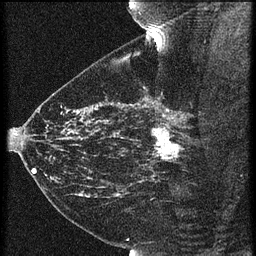
Breast MRI (dynamic contrast-enhanced), one sagittal slice; slice 42 of 60 in the series (ordered by position); 3 images stored at this slice position (order not interpretable as contrast timing); 1.5 T; TE 4.2 ms, TR 21.3 ms; 1.5 mm slice thickness; 256 × 256 image matrix, field of view 180 × 180 mm. Female patient, age 43 years. Case-level facts recorded for this patient, not image findings: setting: breast cancer imaged before/during neoadjuvant chemotherapy; receptor status: HER2-positive.
Annotated regions visible in this slice (semi-automatic segmentation, software-assisted and operator-edited):
- analysis volume of interest (the breast-tissue region the enhancement analysis was run in; not a lesion): bounding box [x1, y1, x2, y2] px = [119, 114, 189, 173]
- tumour enhancement mask (voxels above the 90 % enhancement threshold inside the analysis volume of interest): [152, 116, 180, 161]